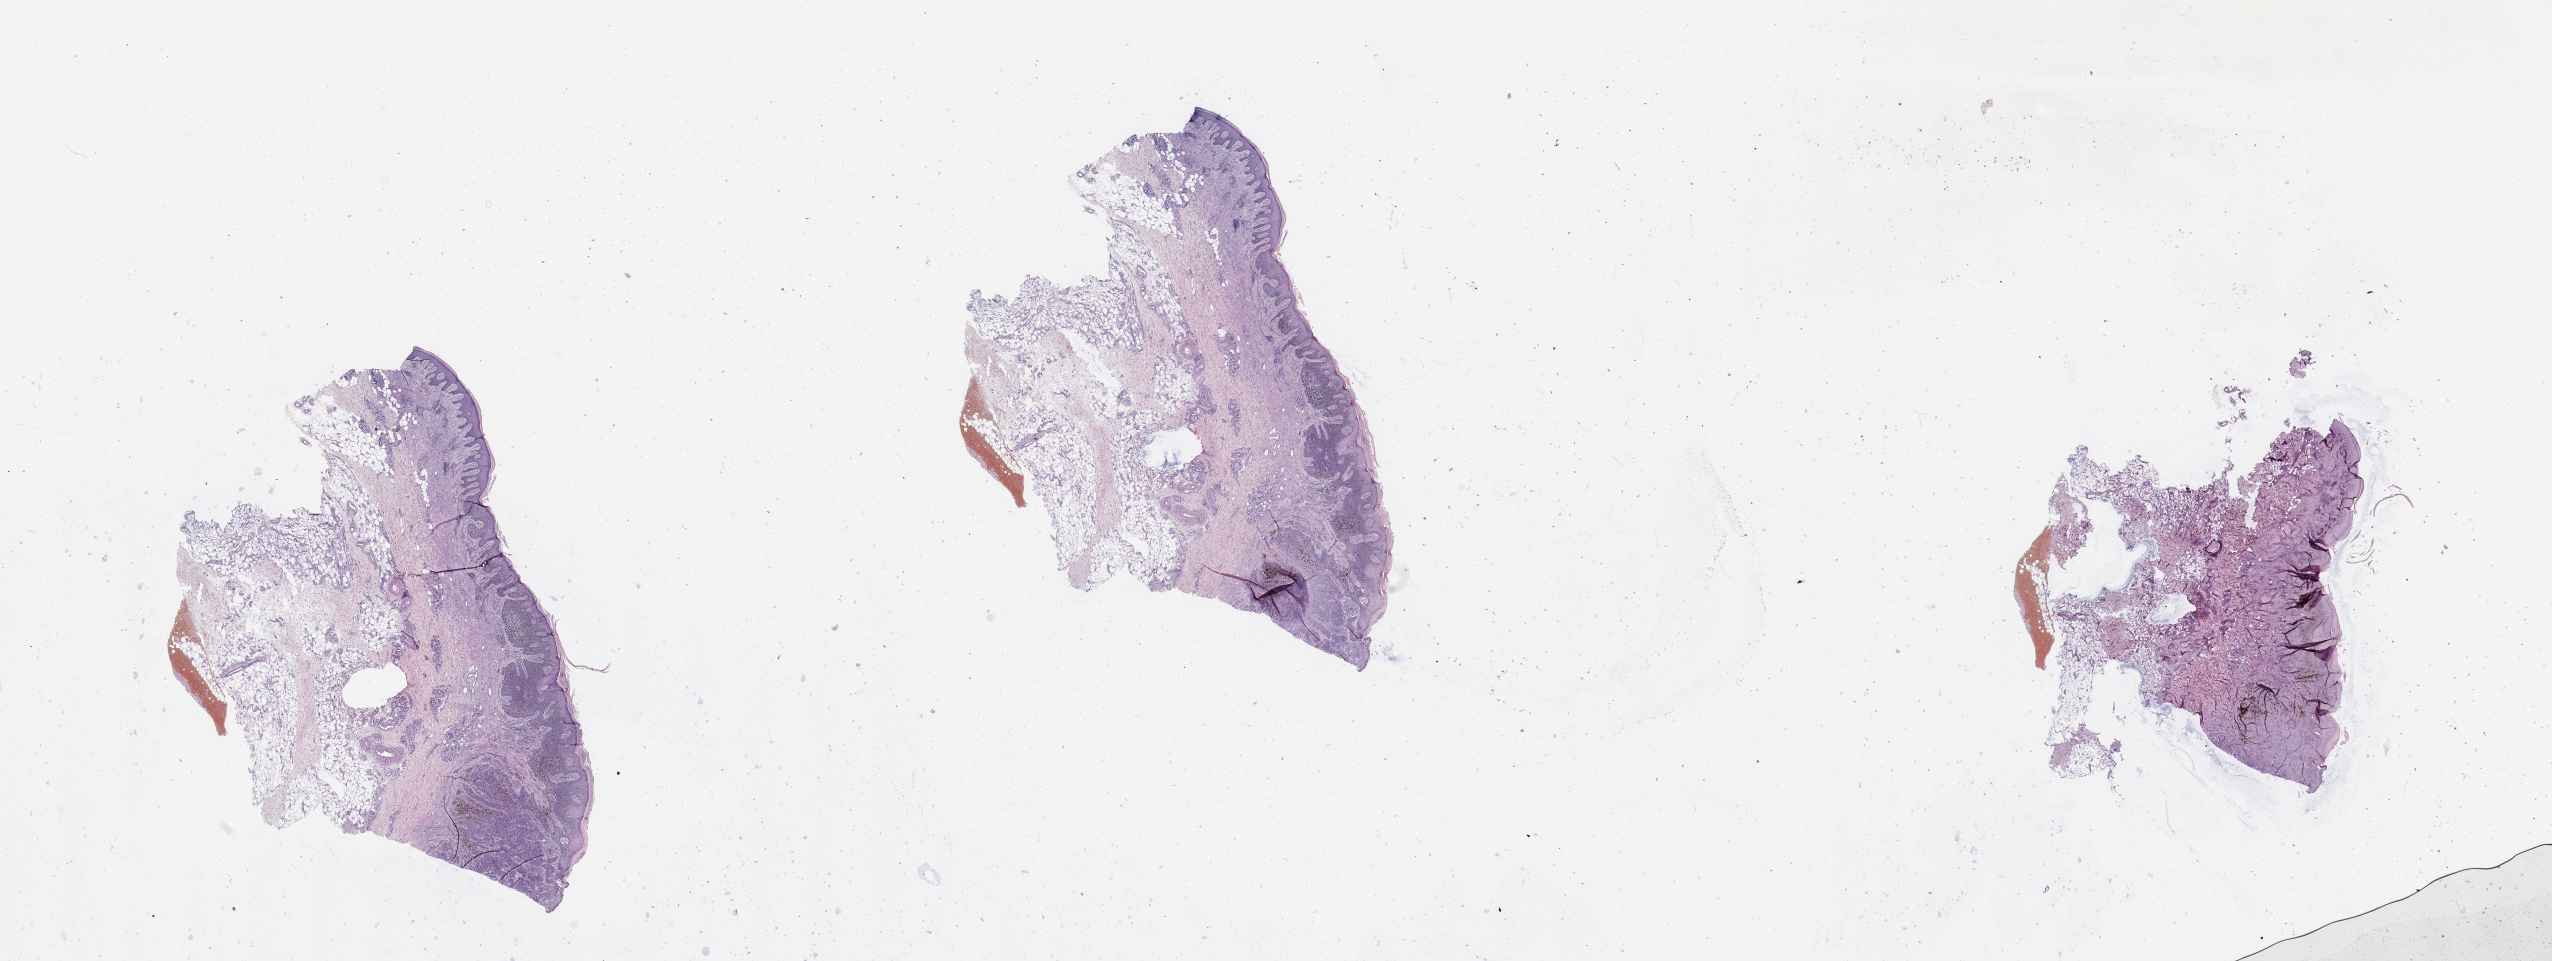
Hematoxylin and eosin (H&E) stained whole-slide image — whole scanned area (about 40.4 x 15.2 mm) shown as a low-resolution overview. Melanoma tumour tissue; sampled site not recorded. Female patient, aged 90 or older.
• AJCC pathologic stage: IIC
• histologic diagnosis: Malignant melanoma, NOS
• primary tumour site (as recorded): extremities